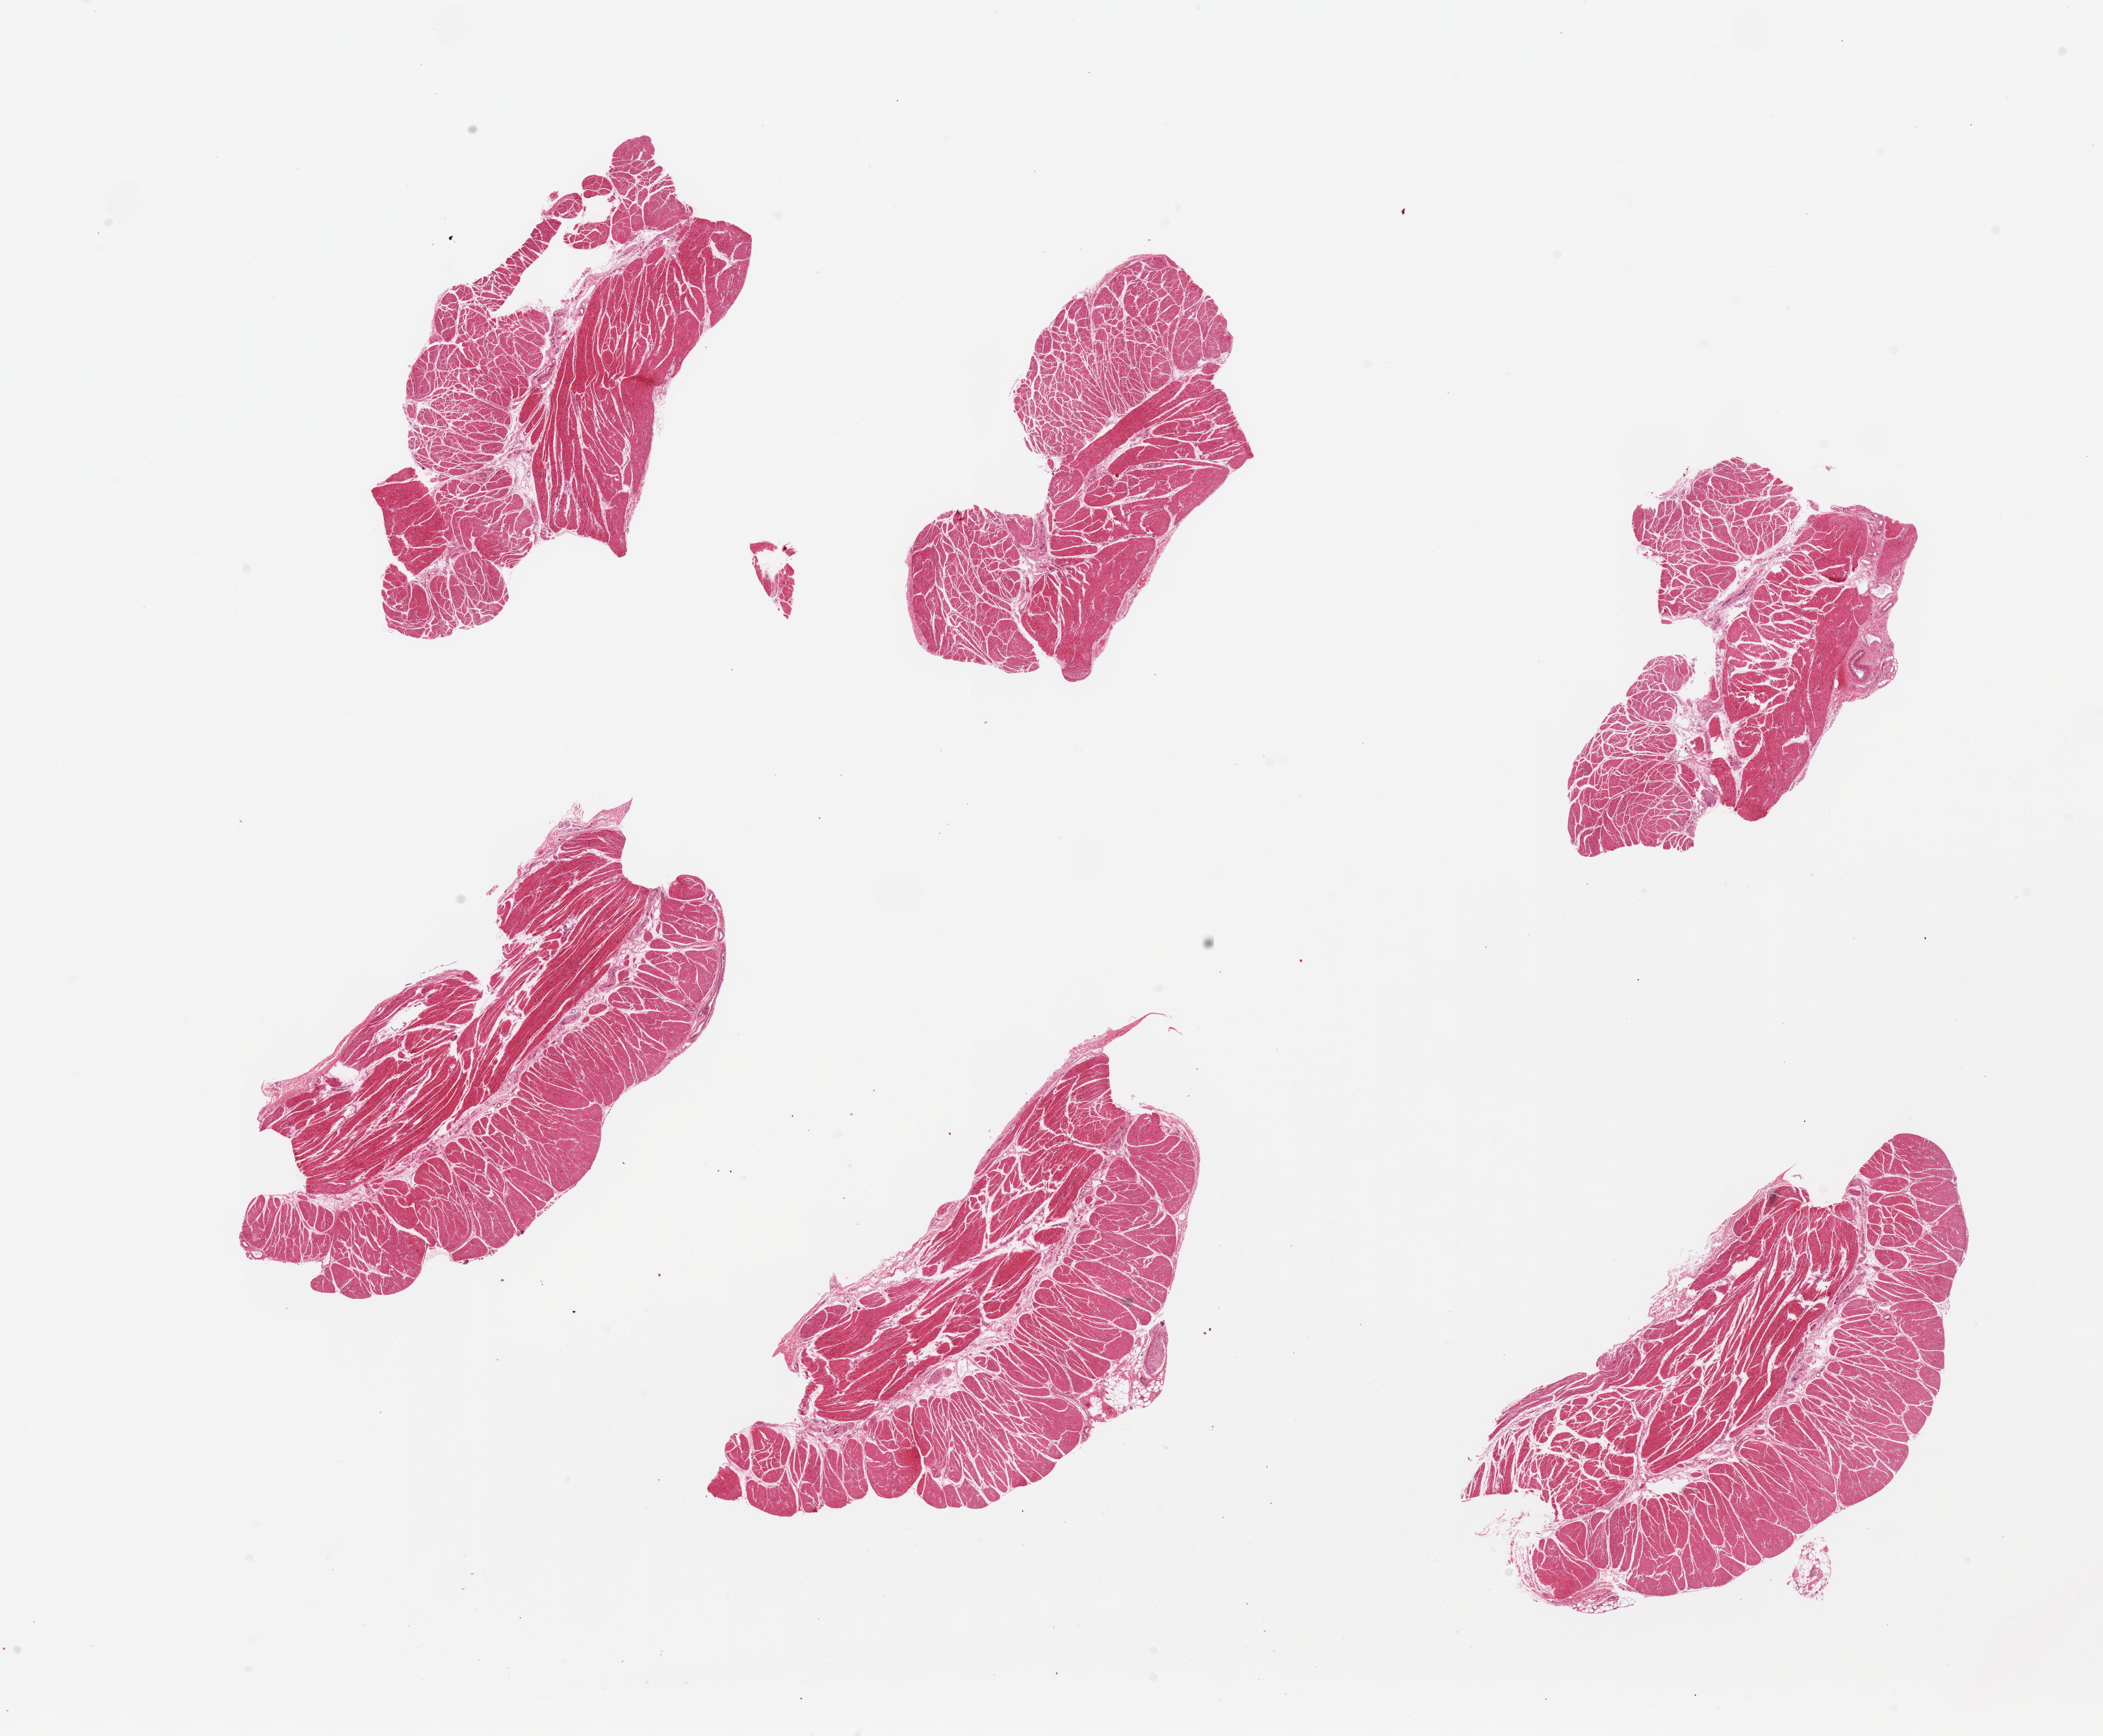
Digitized H&E-stained section, brightfield — whole scanned area (about 25.6 x 21.1 mm, acquisition: 20x scan) shown as a low-resolution overview; PAXgene-fixed, paraffin-embedded tissue; target tissue: esophageal muscle; donor tissue sample. Female donor.
* review note (as recorded): 6 pieces, well trimmed